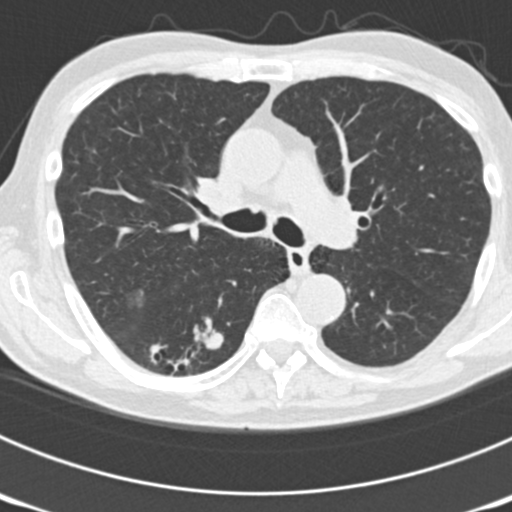
Low-dose screening chest CT, axial slice; third annual screen; lung window (W 1500 / L -600 HU); 2 mm slice thickness; standard (soft-tissue) reconstruction kernel (B30f); 120 kVp; slice 62 of 177 in the series. Male, age 70 years at enrolment. Current smoker at enrolment.
- Lesion marked by an expert reader, bounding box (x1, y1, x2, y2) in pixels: (142, 313, 236, 386).
- The screening reader recorded 3 non-calcified nodules or masses ≥4 mm on this exam; which of them this box marks is not recorded.
- Participant outcome: lung cancer diagnosed 14 days after this screen — bronchiolo-alveolar adenocarcinoma, NOS, right lower lobe, poorly differentiated (G3), stage IB (AJCC 6th edition), 30 mm at pathology.